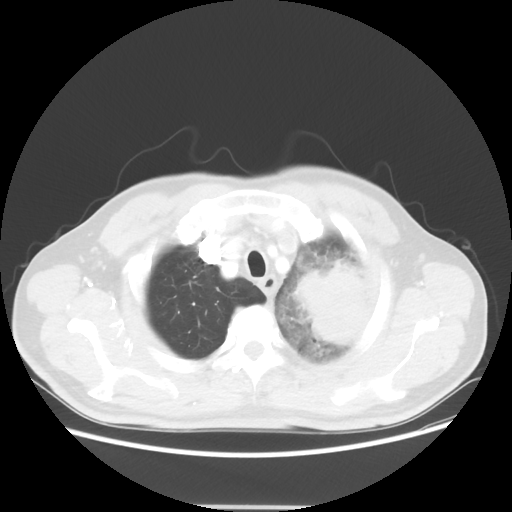
Chest CT, one axial slice; slice 48 of 53 in the series (ordered by position); 100 kVp; lung window (W 1500 / L -600 HU); 5 mm slice thickness; 512 × 512 image matrix, field of view 391 × 391 mm. Patient: male, 60 years. Case-level facts recorded for this patient, not image findings: clinical TNM (as recorded): T4 N1 M1a; histopathological grade: G3.
Structures marked on this image (rectangle marked by the reading radiologist):
- lung tumour (recorded histology: large cell carcinoma): bounding box [x1, y1, x2, y2] px = [278, 256, 383, 365]